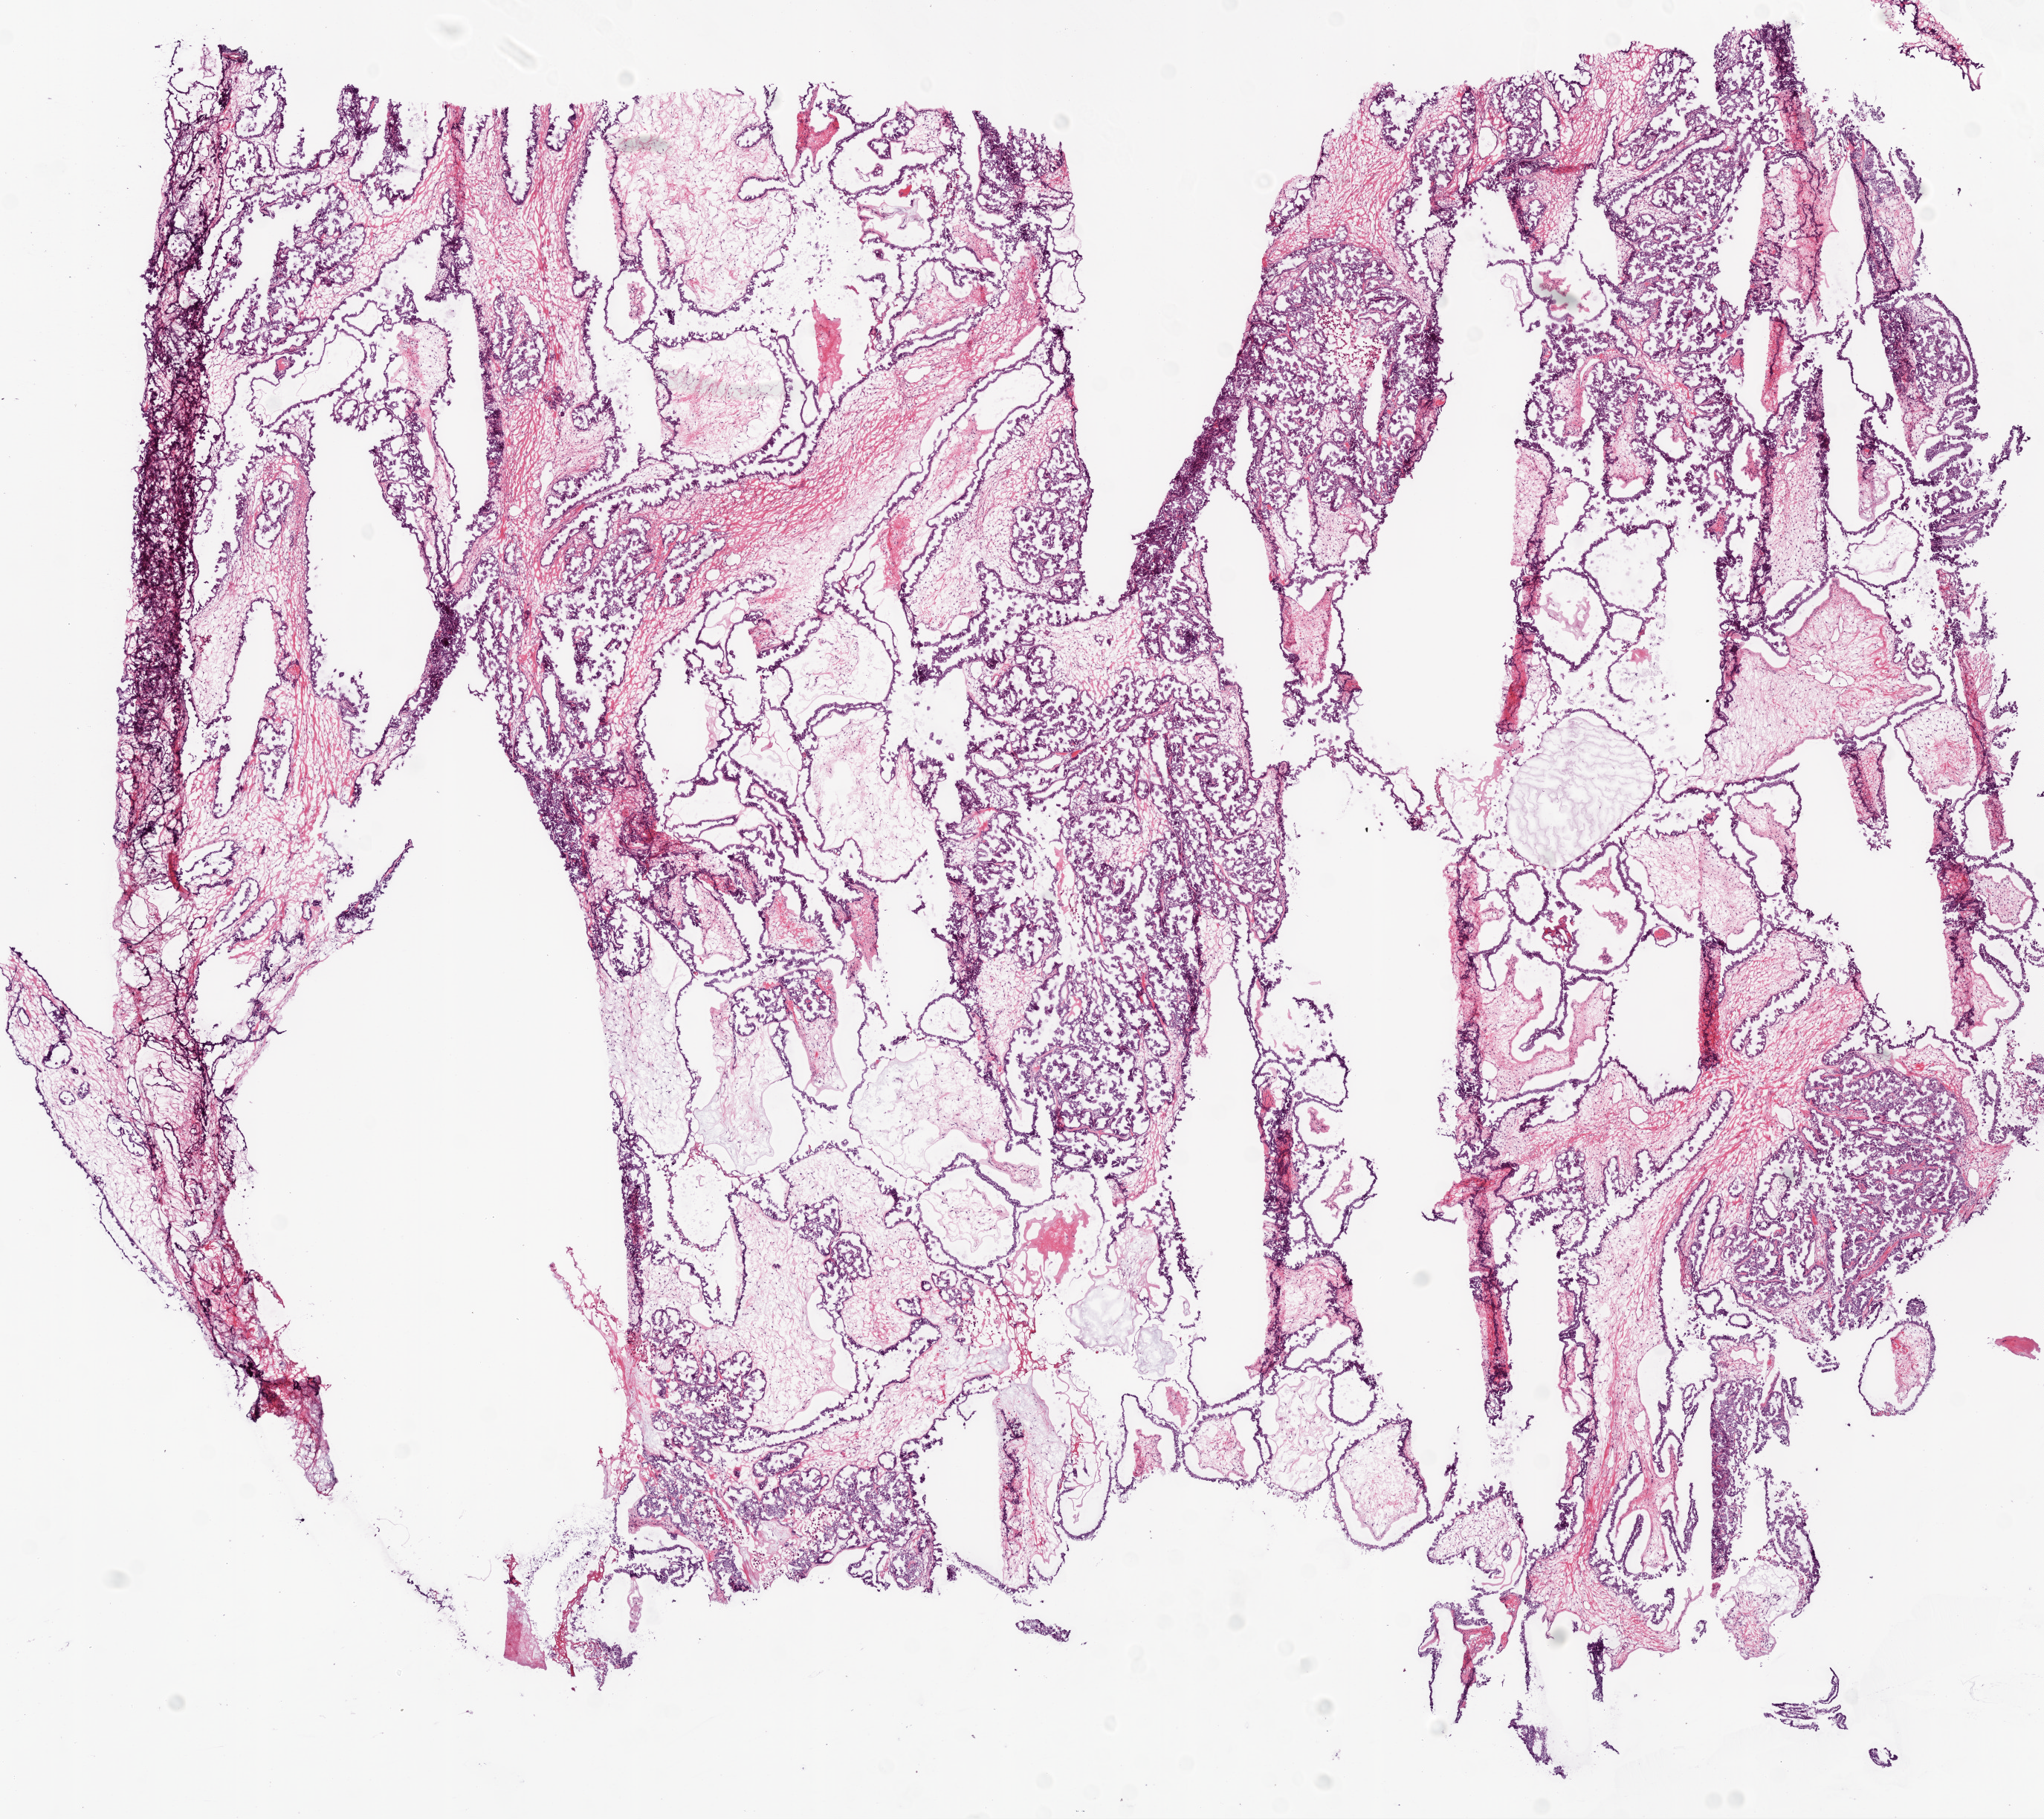
Hematoxylin and eosin (H&E) stained whole-slide image, a low-resolution overview of the entire scanned area, about 11.0 x 9.8 mm (acquisition: 20x scan); frozen section from the bottom of the tissue portion; primary tumour sample from the ovary. Patient: female, age at initial diagnosis 75 years. Histologic grade: G3 (poorly differentiated). Composition of this section per pathologist review: tumour cells 84%, tumour nuclei 85%, normal cells 0%, stromal cells 15%, necrosis 1%.
- FIGO stage: IIIC
- diagnosis: Serous cystadenocarcinoma, NOS